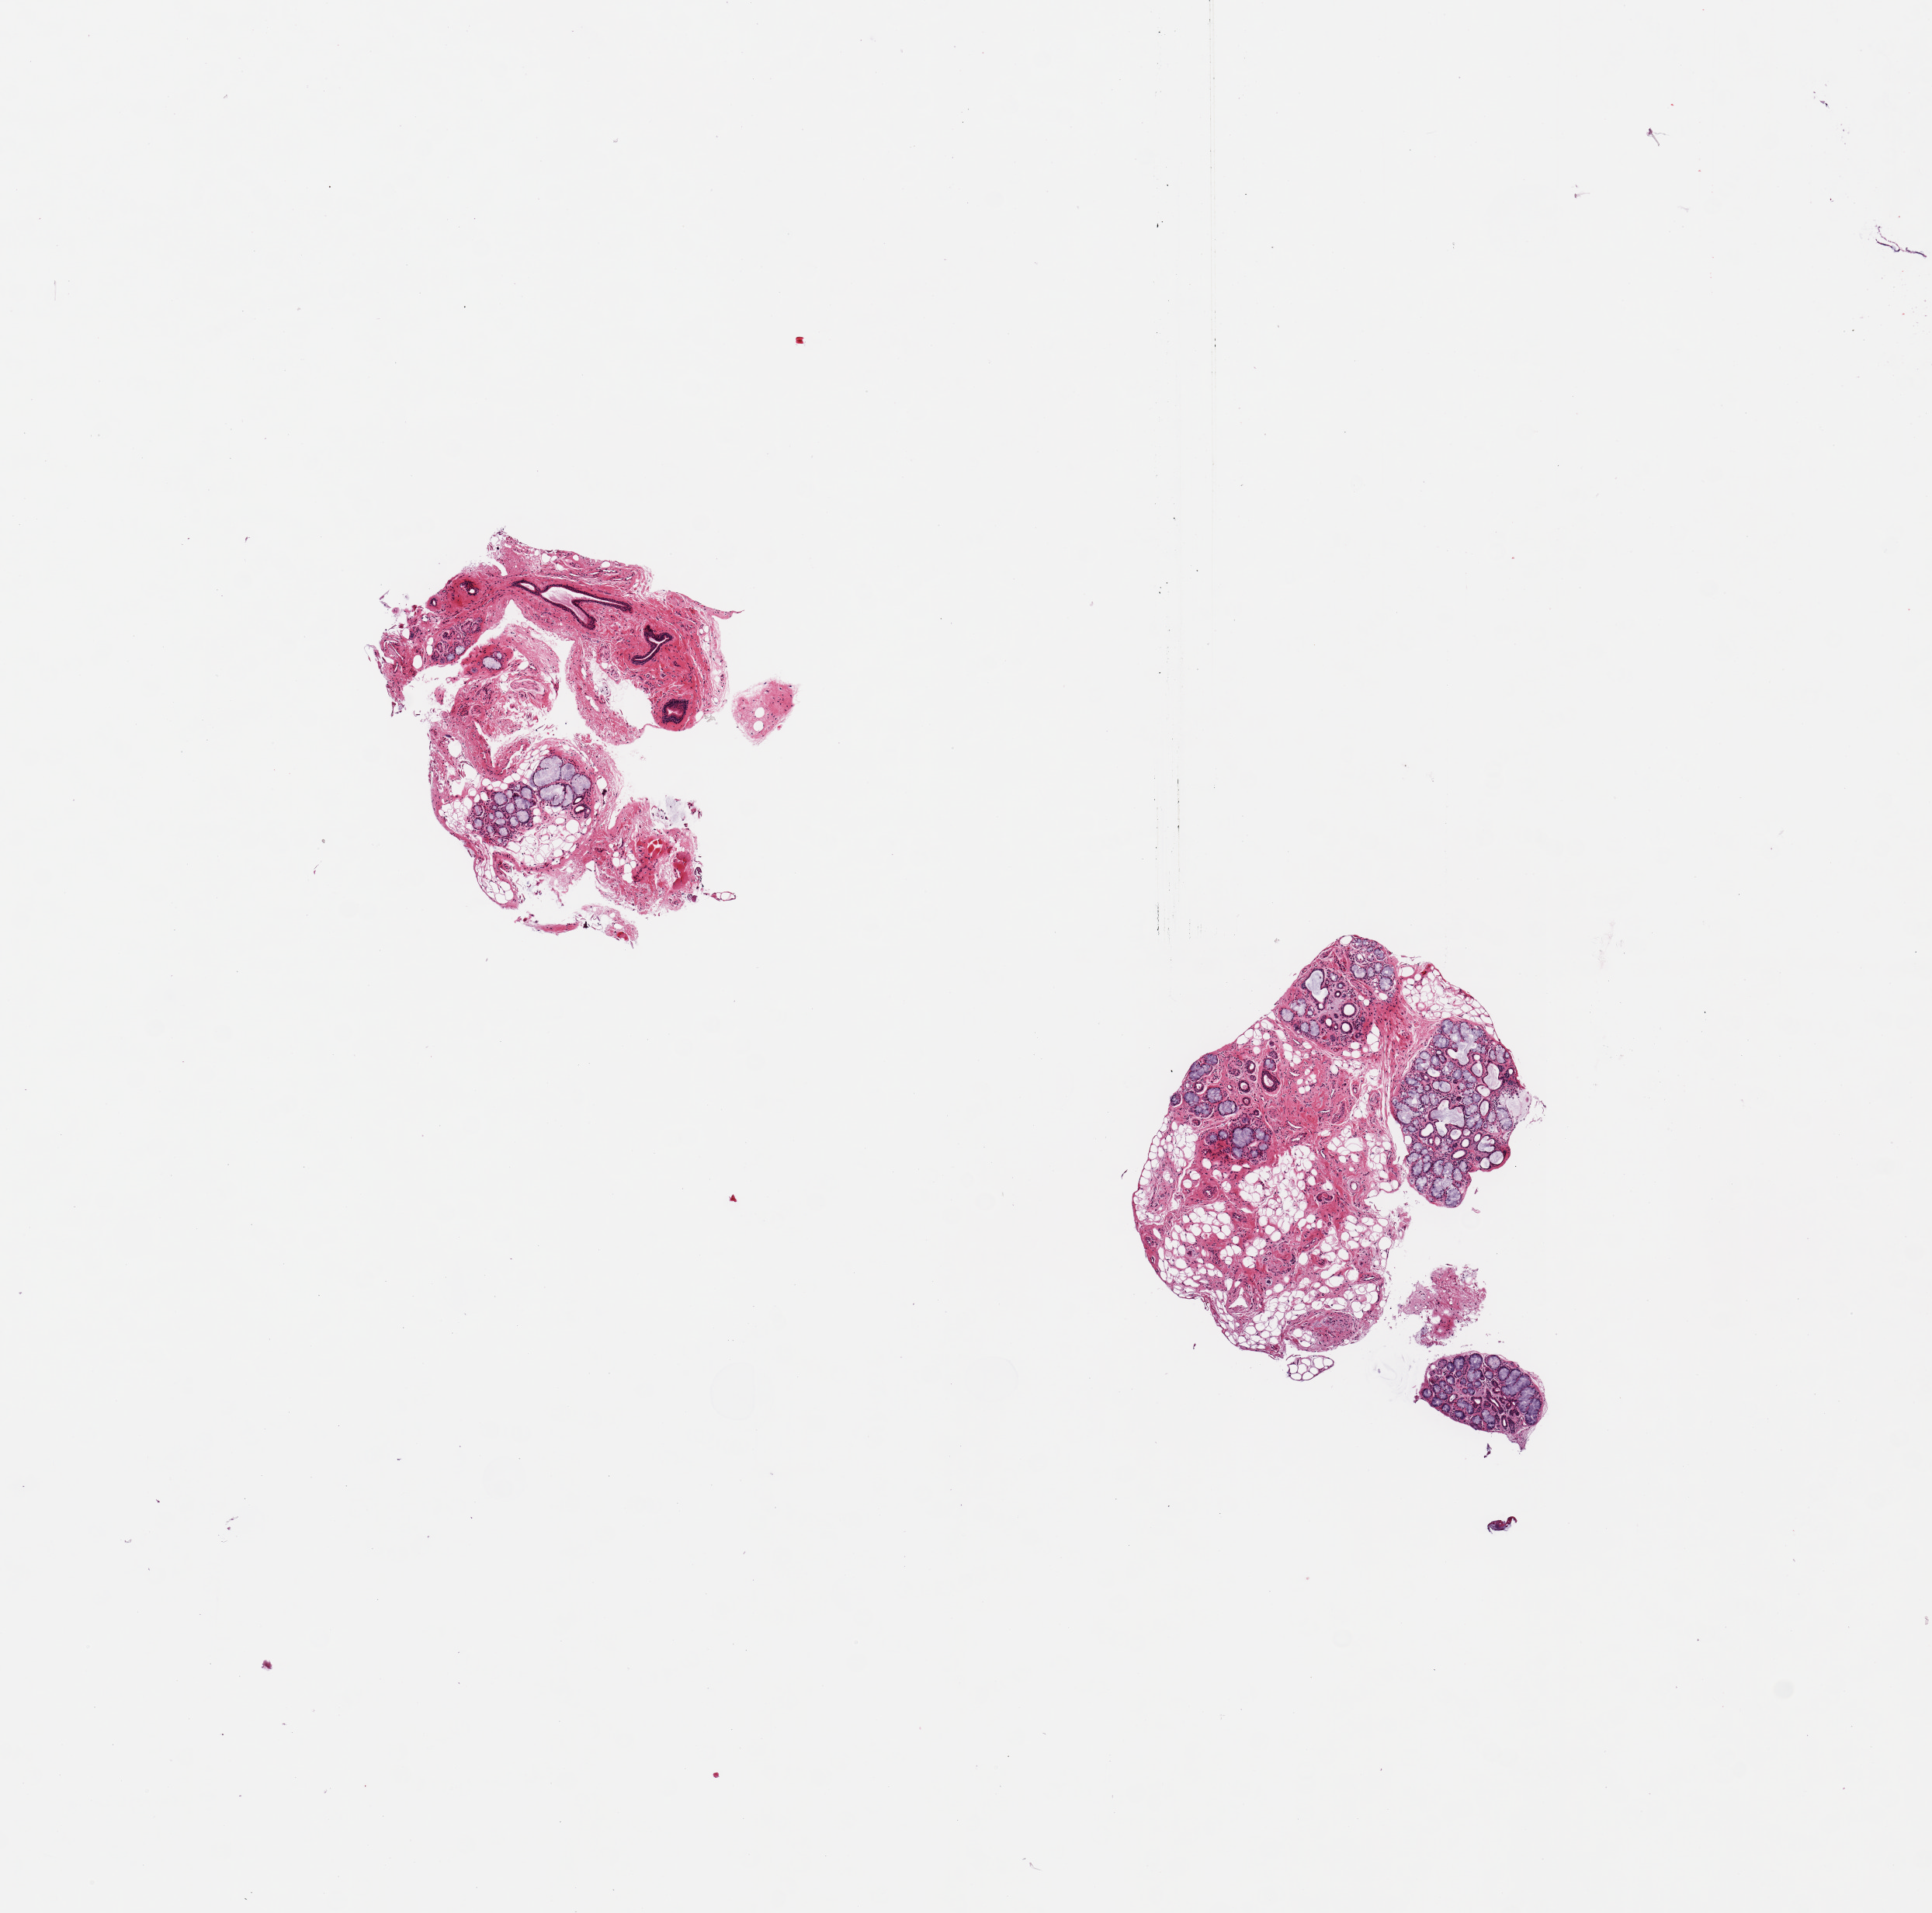
Digitized H&E-stained section — a low-resolution overview of the entire scanned area, about 9.8 x 9.7 mm (slide scanned at 20x), PAXgene-fixed, paraffin-embedded tissue, sampled site (target tissue): minor salivary gland, tissue donor sample. Female donor.
Reviewer comment on this tissue sample: 2 pieces; 20% and 60% of glandular component surrounded by fibroadipose and vascular tissue; ductal elements.